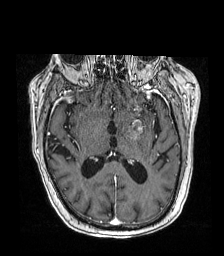
Brain MRI from a brain-tumour surgery series, one axial slice. Slice 89 of 192 in the series (ordered by position). T1-weighted post-contrast. 224 × 256 image matrix, field of view 219 × 250 mm. Case-level facts recorded for this patient, not image findings: histopathology: Metastatic carcinoma from lung primary.
Outlined on this slice (outlined manually by an expert reader):
- tumour: bounding box (x1, y1, x2, y2) in pixels: (125, 116, 140, 136)